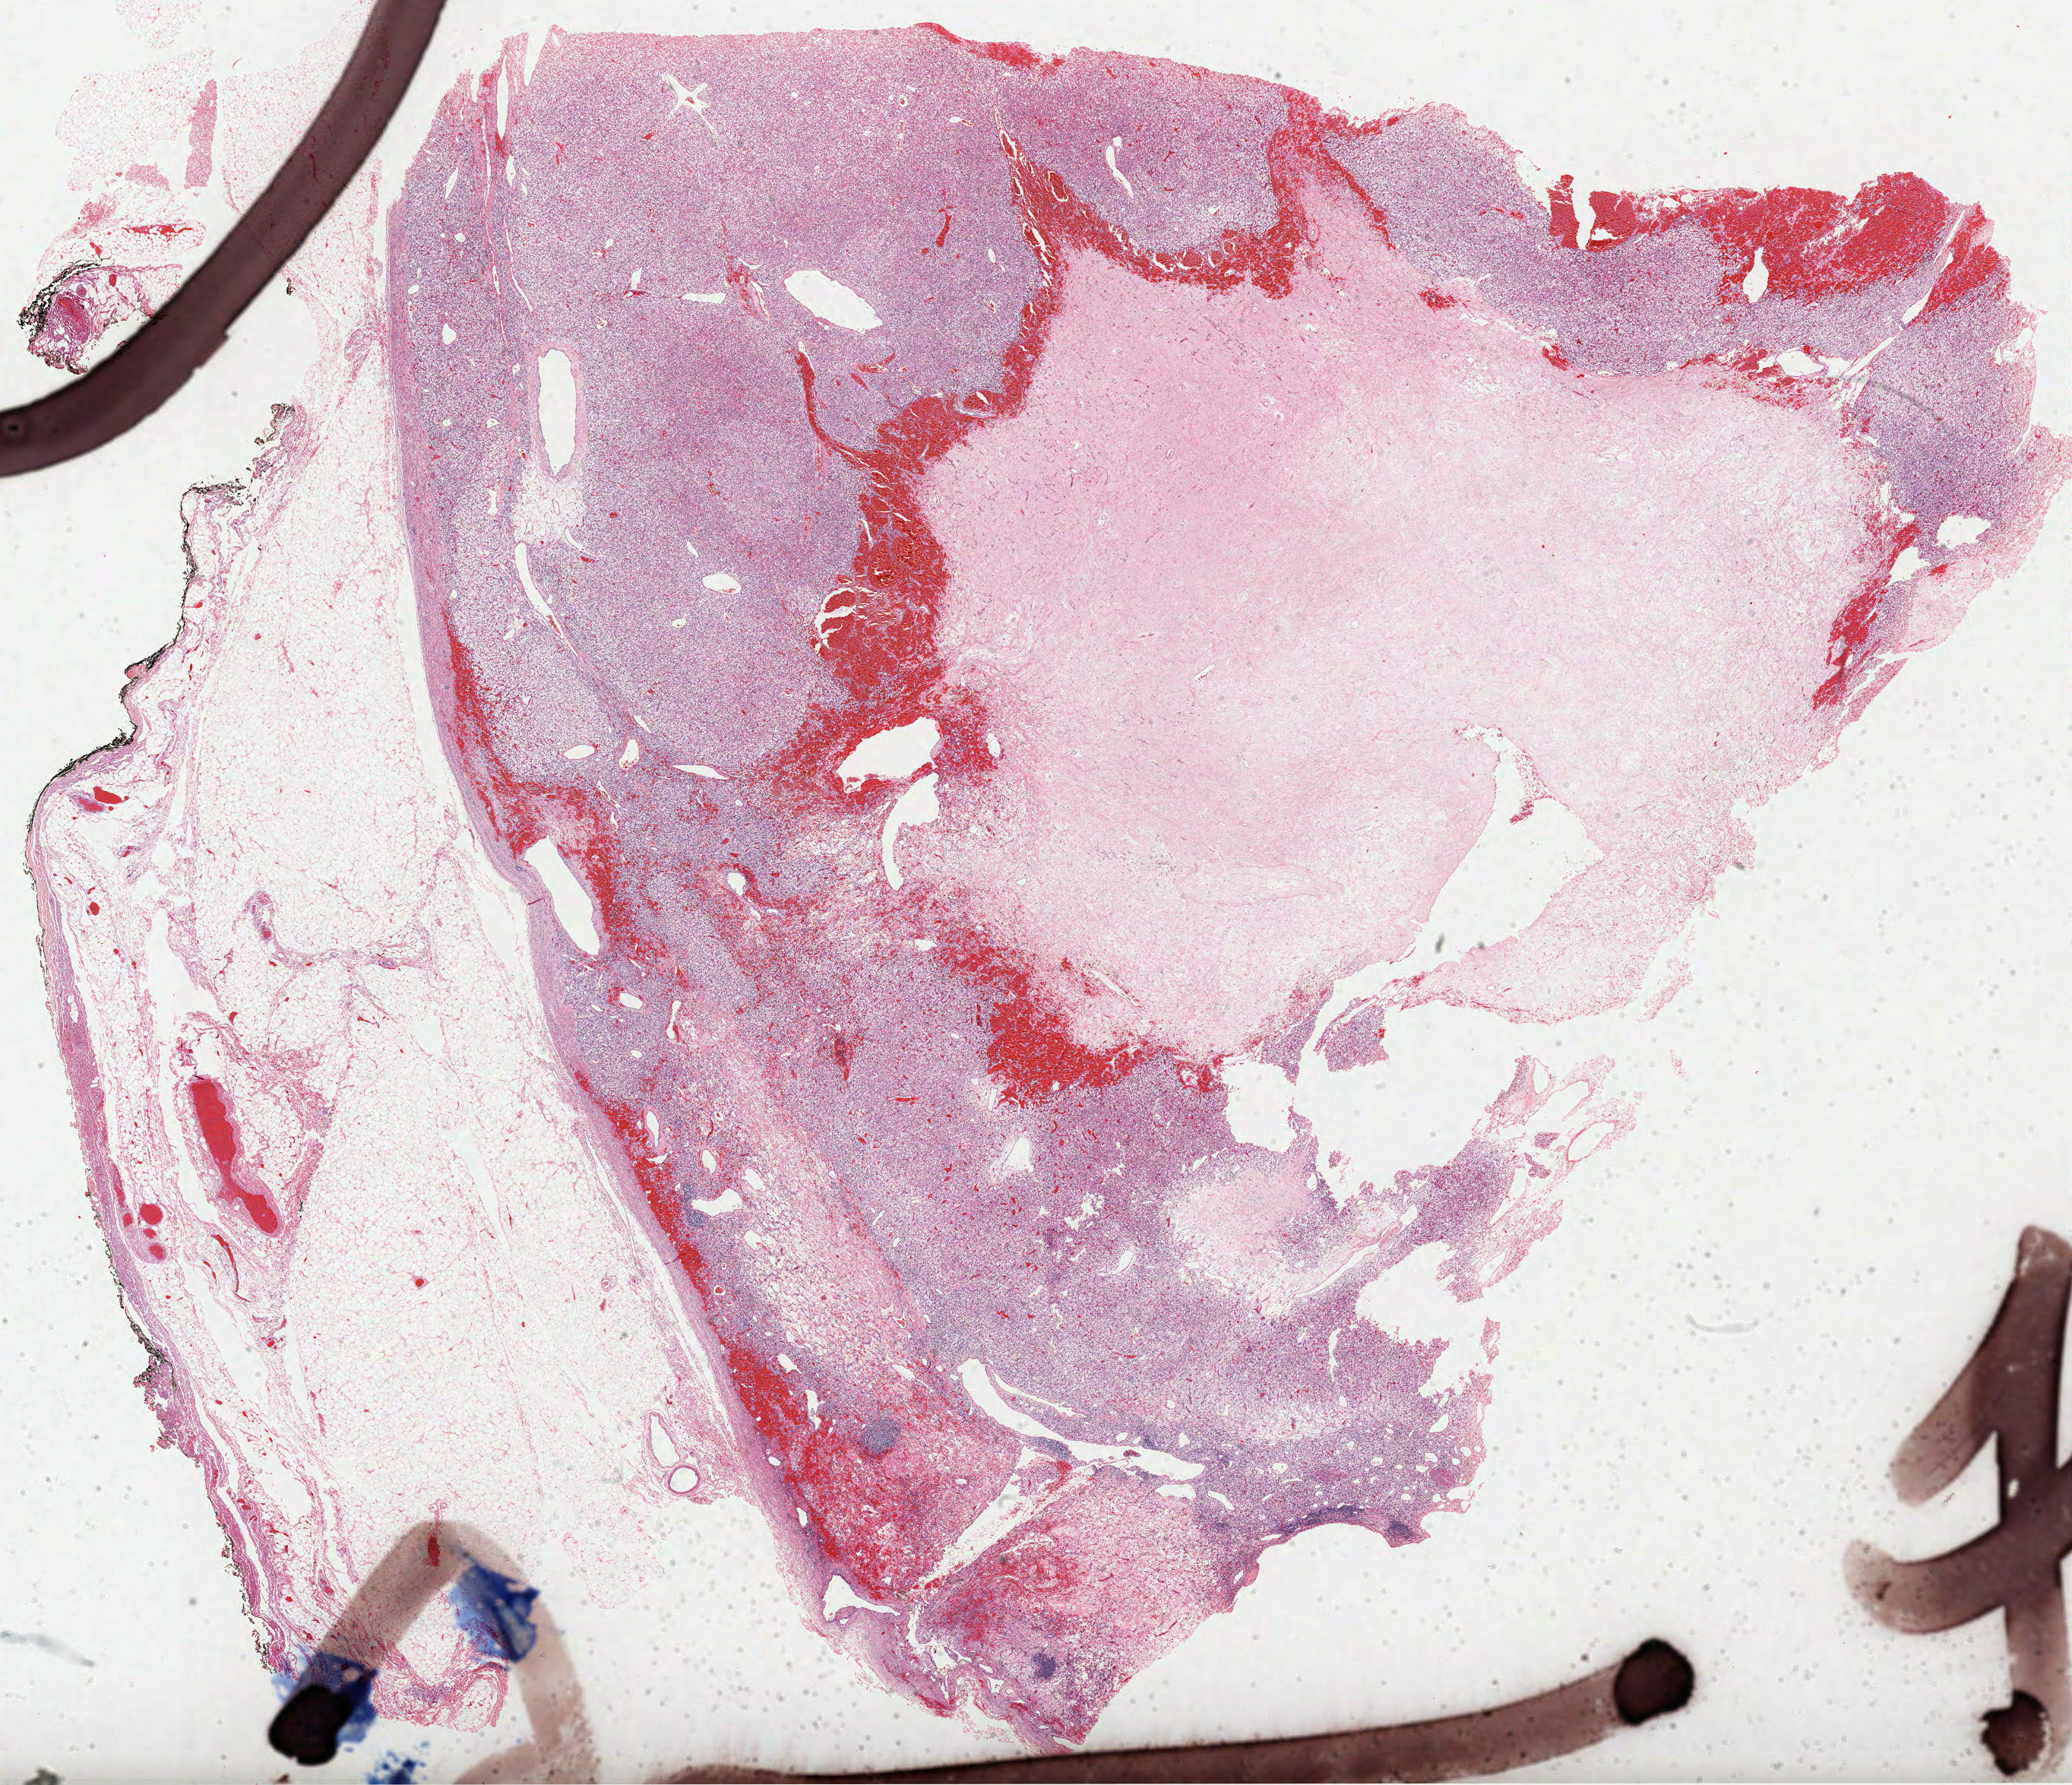
Digitized Hematoxylin and eosin (H&E) stained tissue section (whole slide), low-resolution overview of the scanned area, about 22.0 x 18.9 mm, formalin-fixed paraffin-embedded (FFPE) diagnostic section, sample: primary tumour, kidney. Female patient. Histologic grade: G2 (moderately differentiated).
• laterality: left
• pathologic diagnosis: Clear cell adenocarcinoma, NOS
• AJCC pathologic stage: I